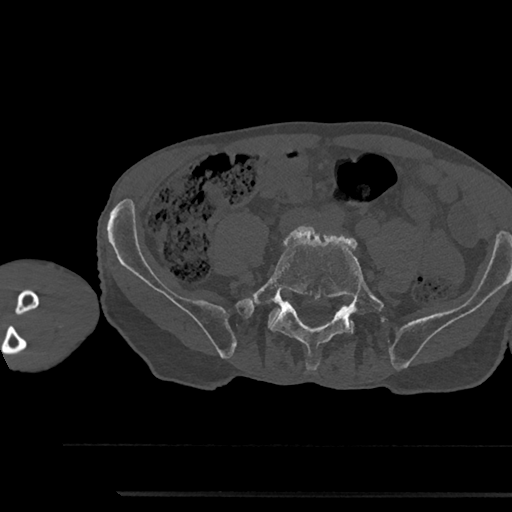
CT including the spine, one axial slice. Position 345 of 797 along the scan axis. Reconstruction kernel Br40s/3. Bone window (W 1800 / L 400 HU). 0.5 mm slice thickness. 512 × 512 image matrix. Patient: male, 79 years. Case-level facts recorded for this patient, not image findings: primary cancer: prostate.
Annotated regions visible in this slice (semi-automatic segmentation, software-assisted and operator-edited):
- L5 vertebra: bounding box (x1, y1, x2, y2) in pixels: (247, 226, 384, 370)